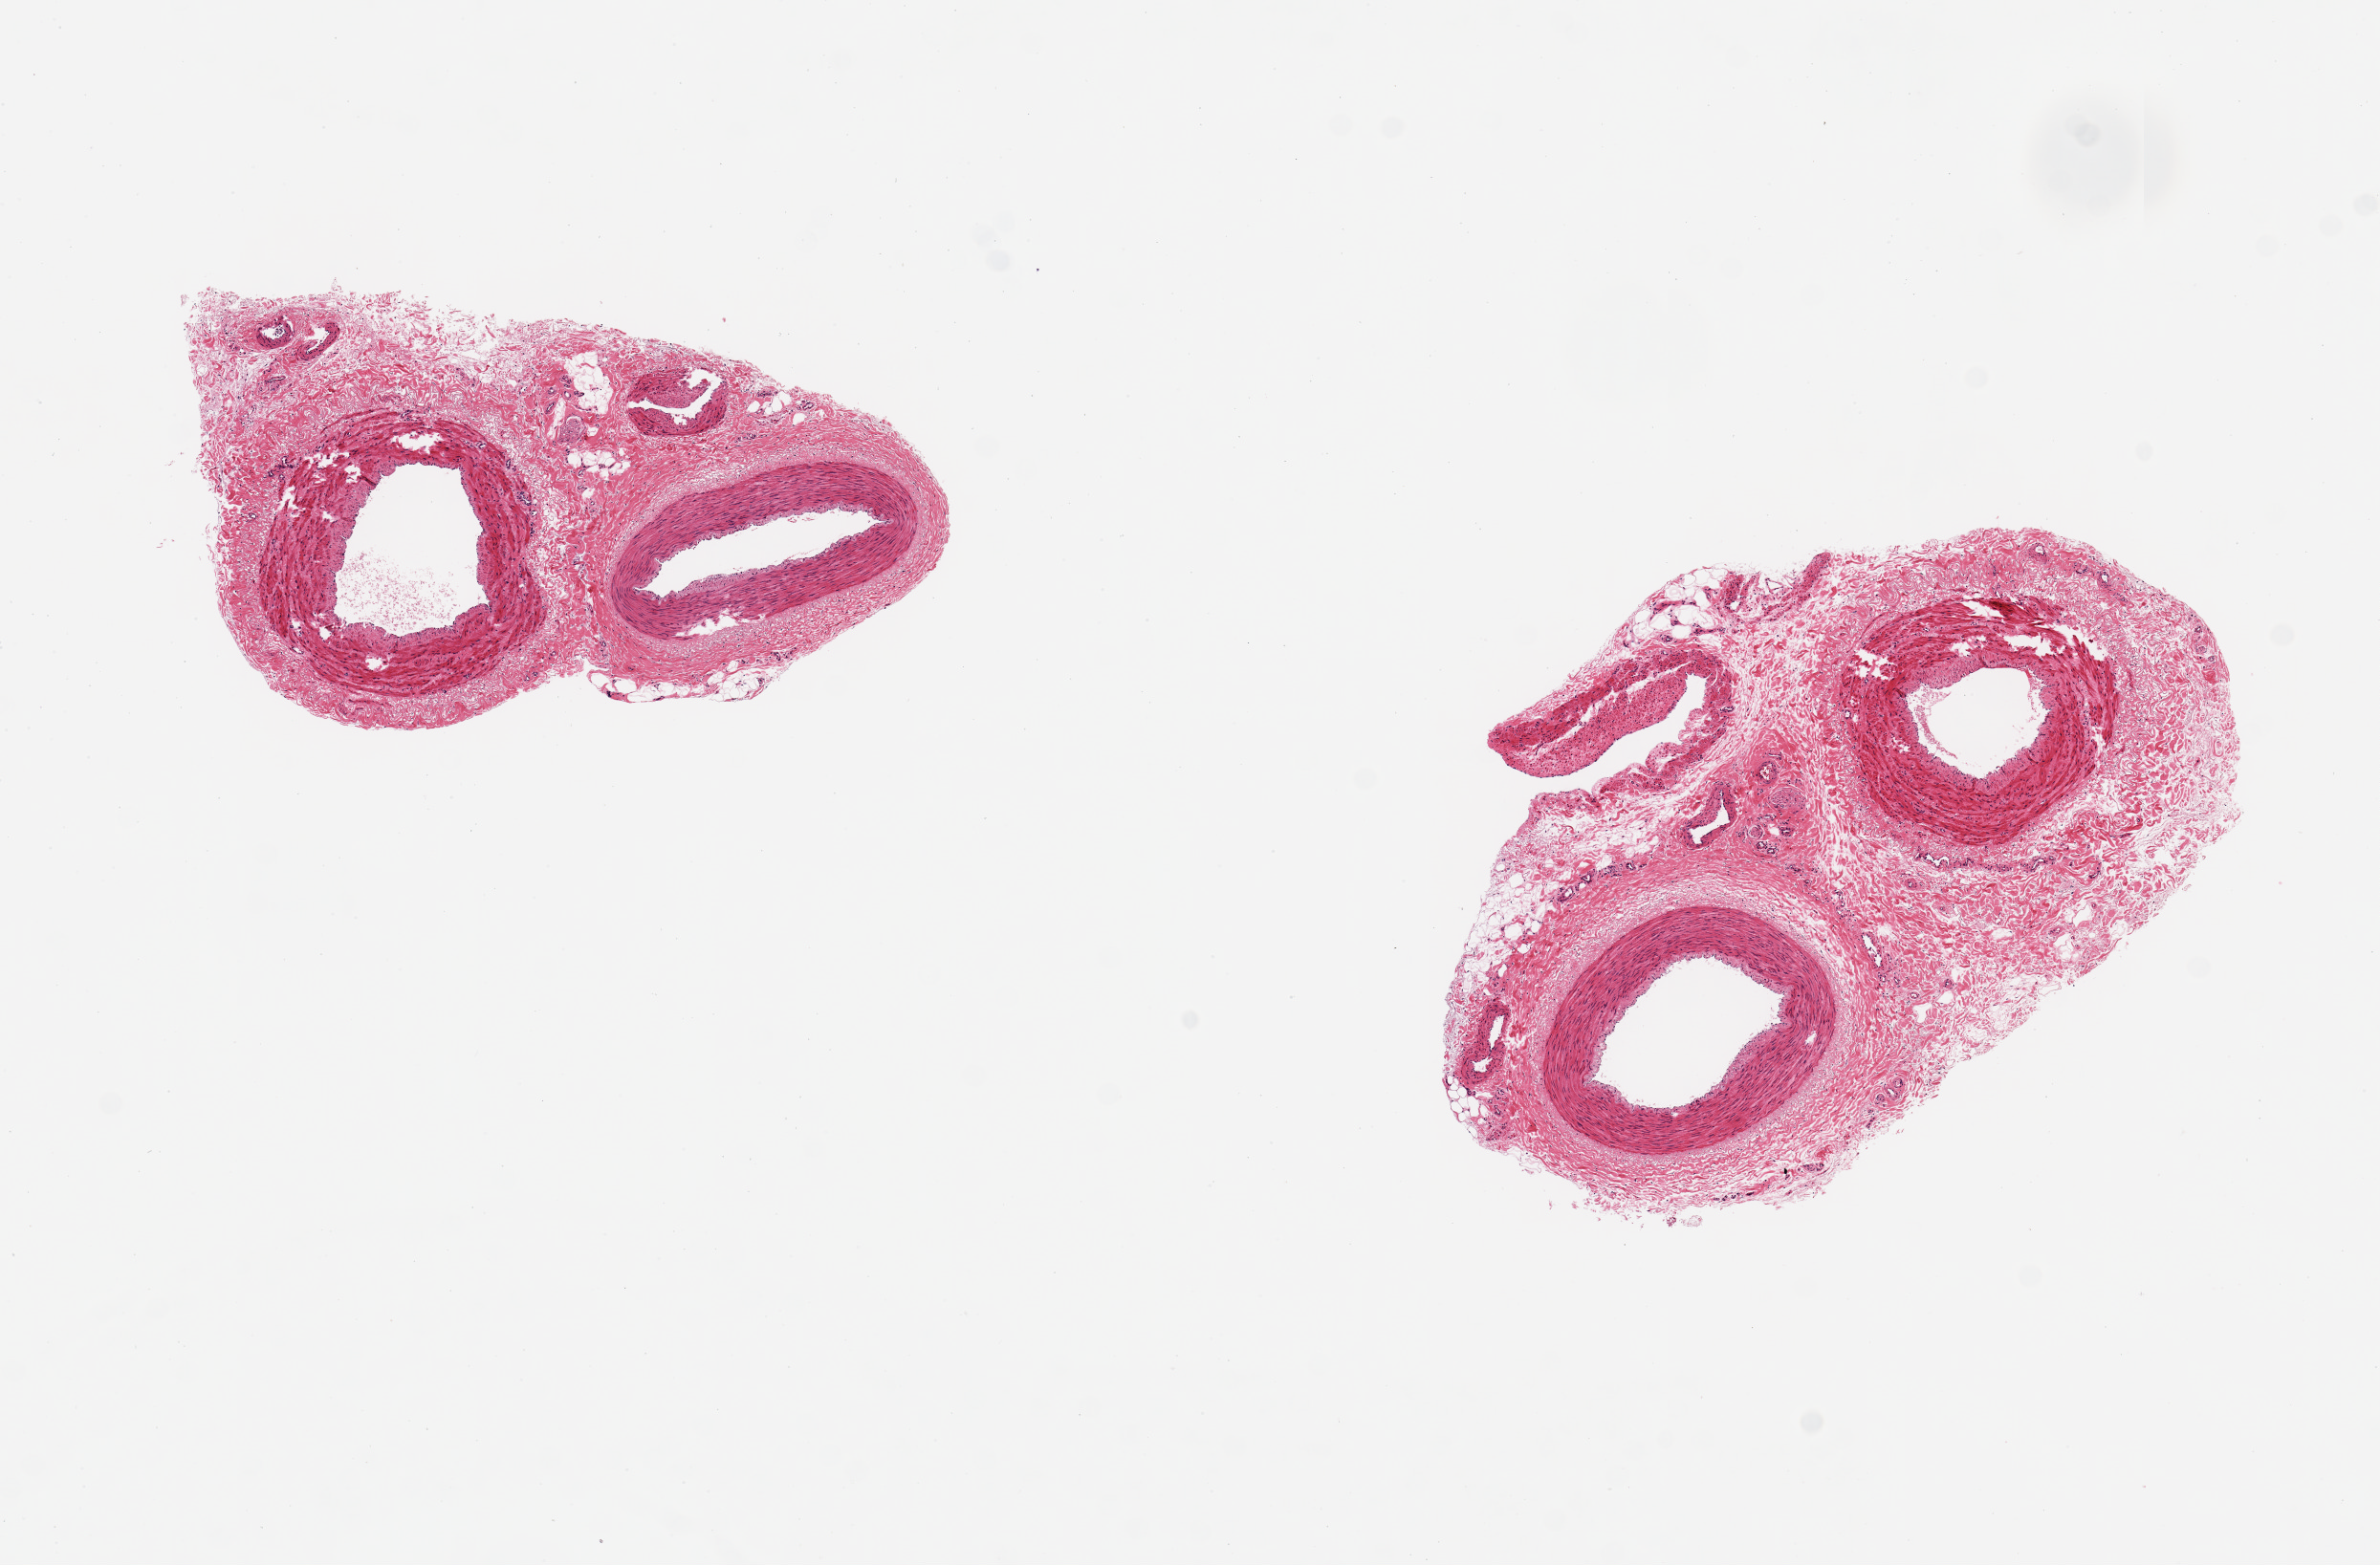
Whole-slide image, haematoxylin and eosin stain — a low-resolution overview of the entire scanned area, about 9.8 x 6.5 mm. PAXgene-fixed paraffin-embedded (PFPE) section. Section of tibial artery (target tissue). Donor tissue sample. Donor: male.
Review note (as recorded): 2 pieces ~3x2 mm; 2 arteries and 1 vein; tissue tears (histologic); embedded in ~40% stroma.